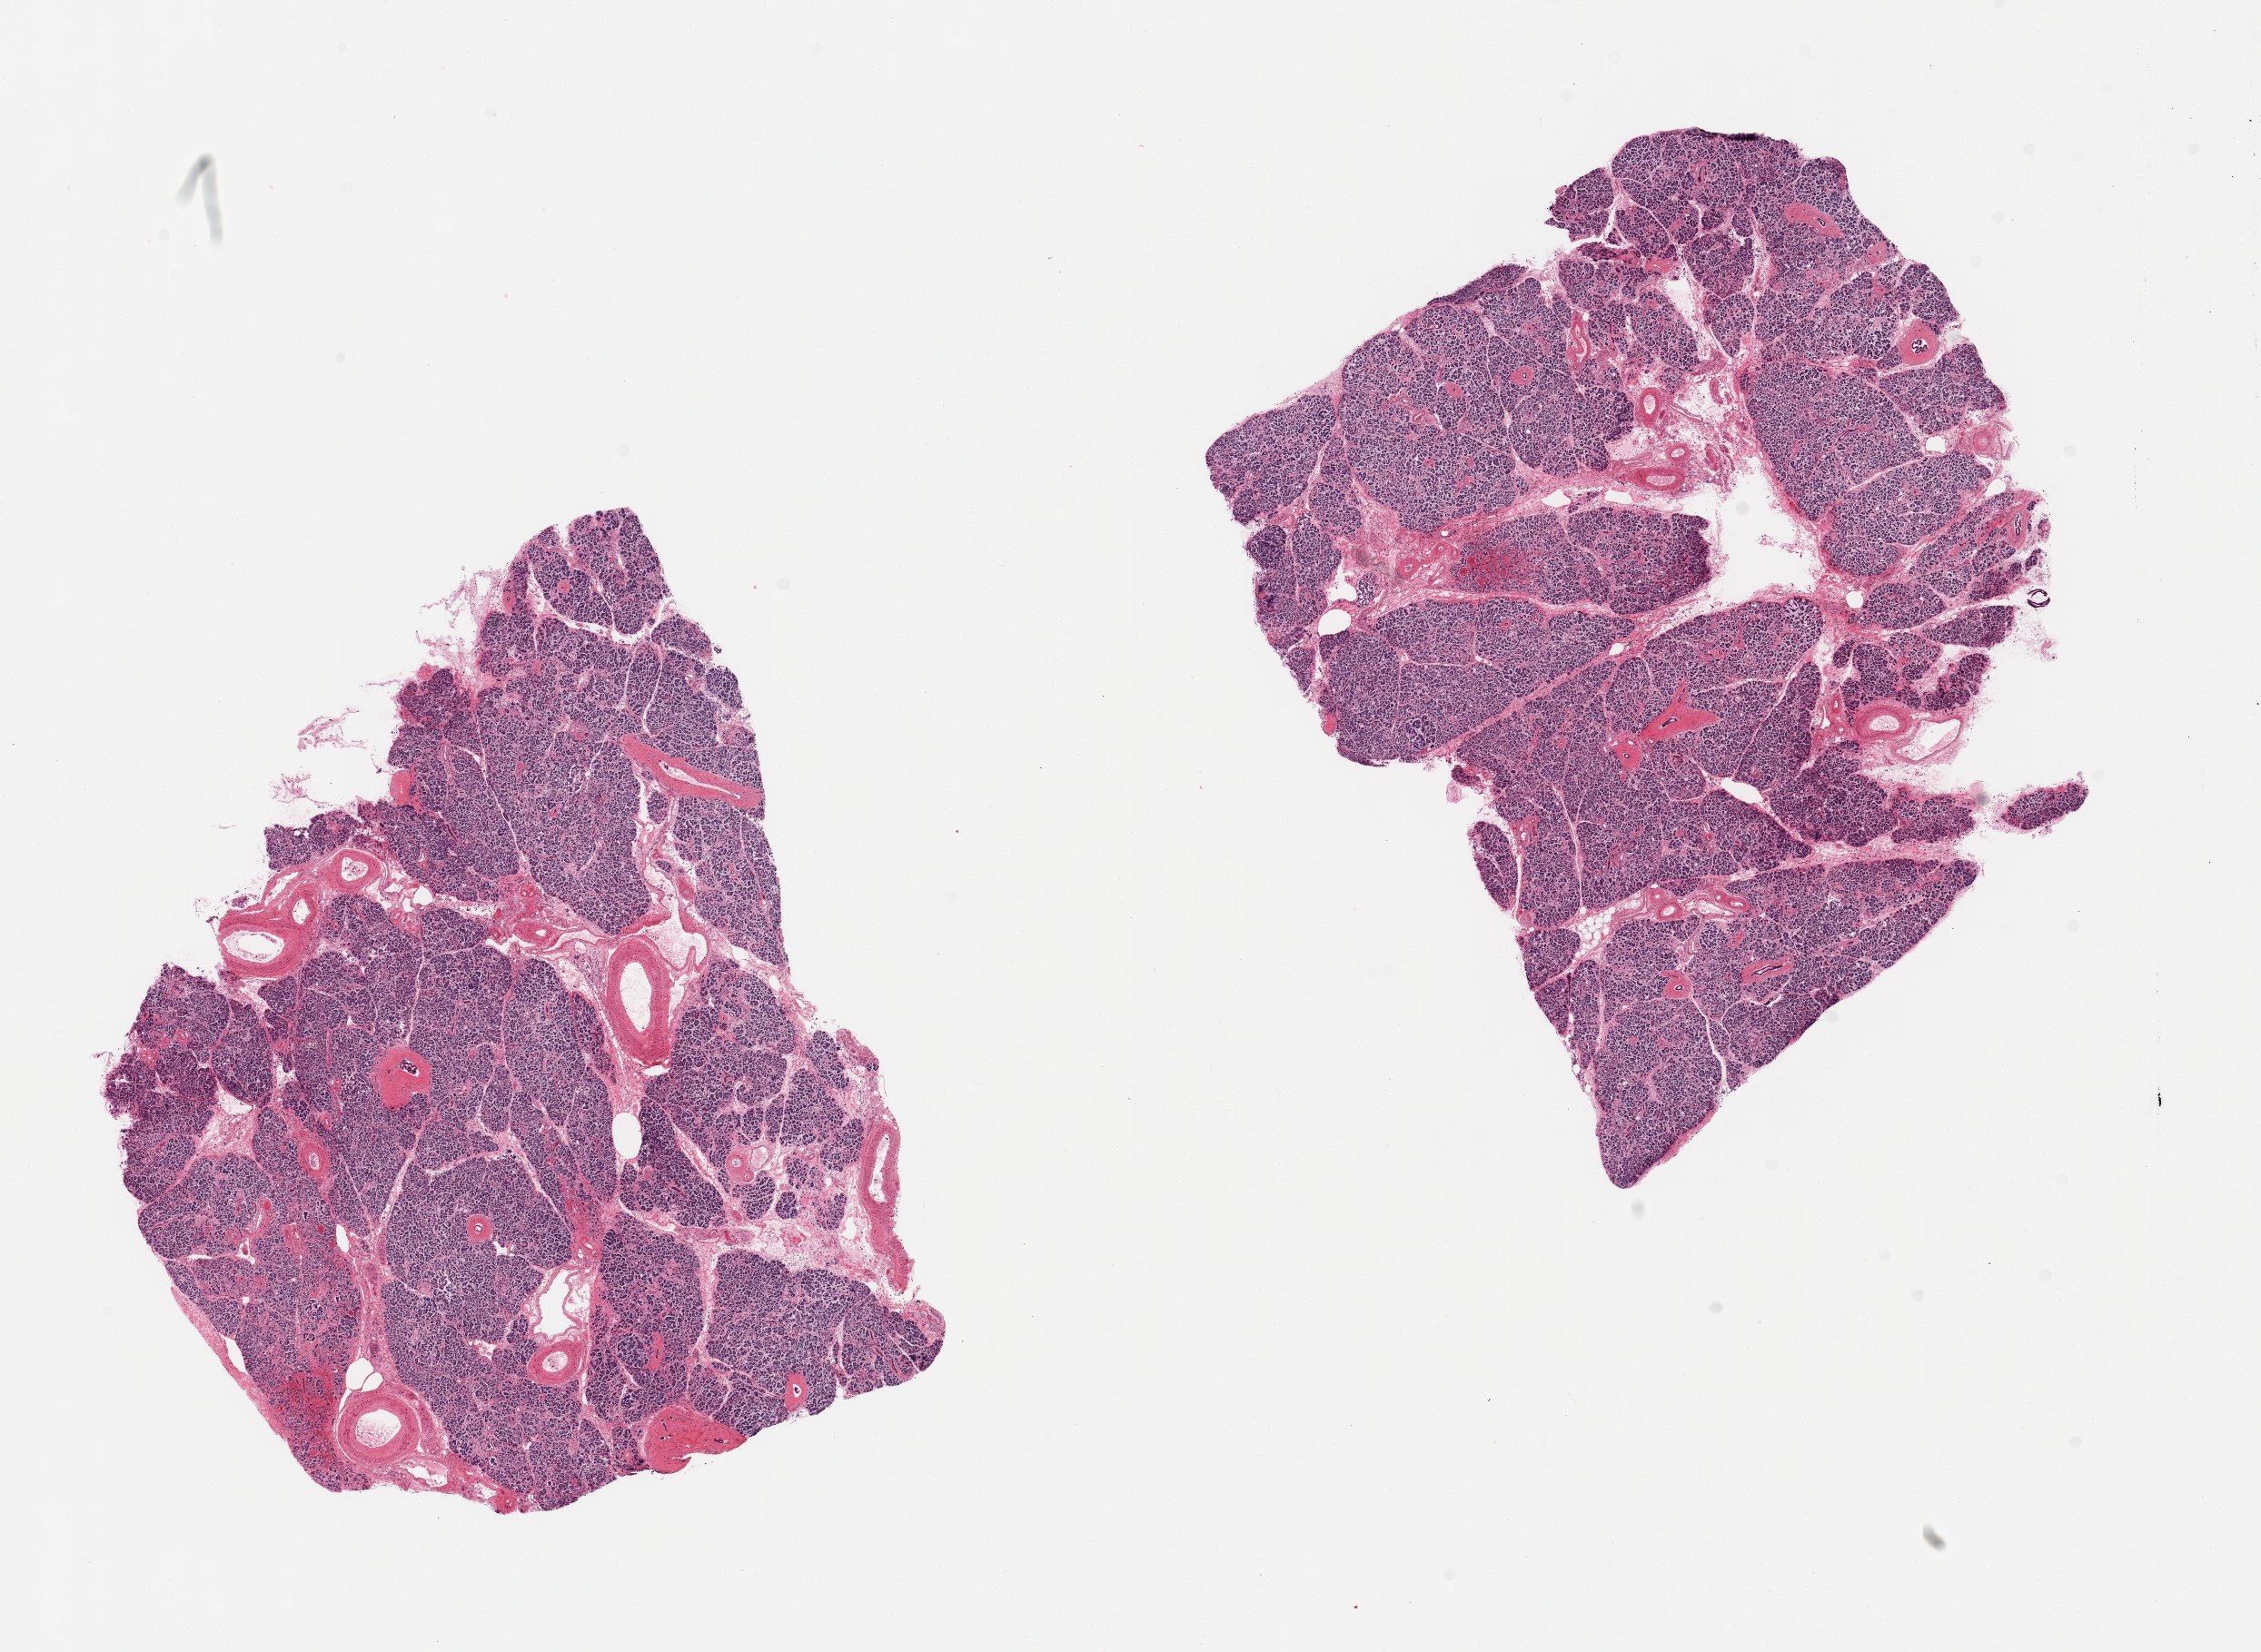
Digitized hematoxylin and eosin (H&E)-stained section, brightfield — a low-resolution overview of the entire scanned area, about 19.7 x 14.4 mm; PAXgene-fixed, paraffin-embedded tissue; section of pancreas (target tissue); donor tissue sample. Male donor.
Review note (as recorded): 2 pieces, moderately advanced saponification. Islets not well visualized.